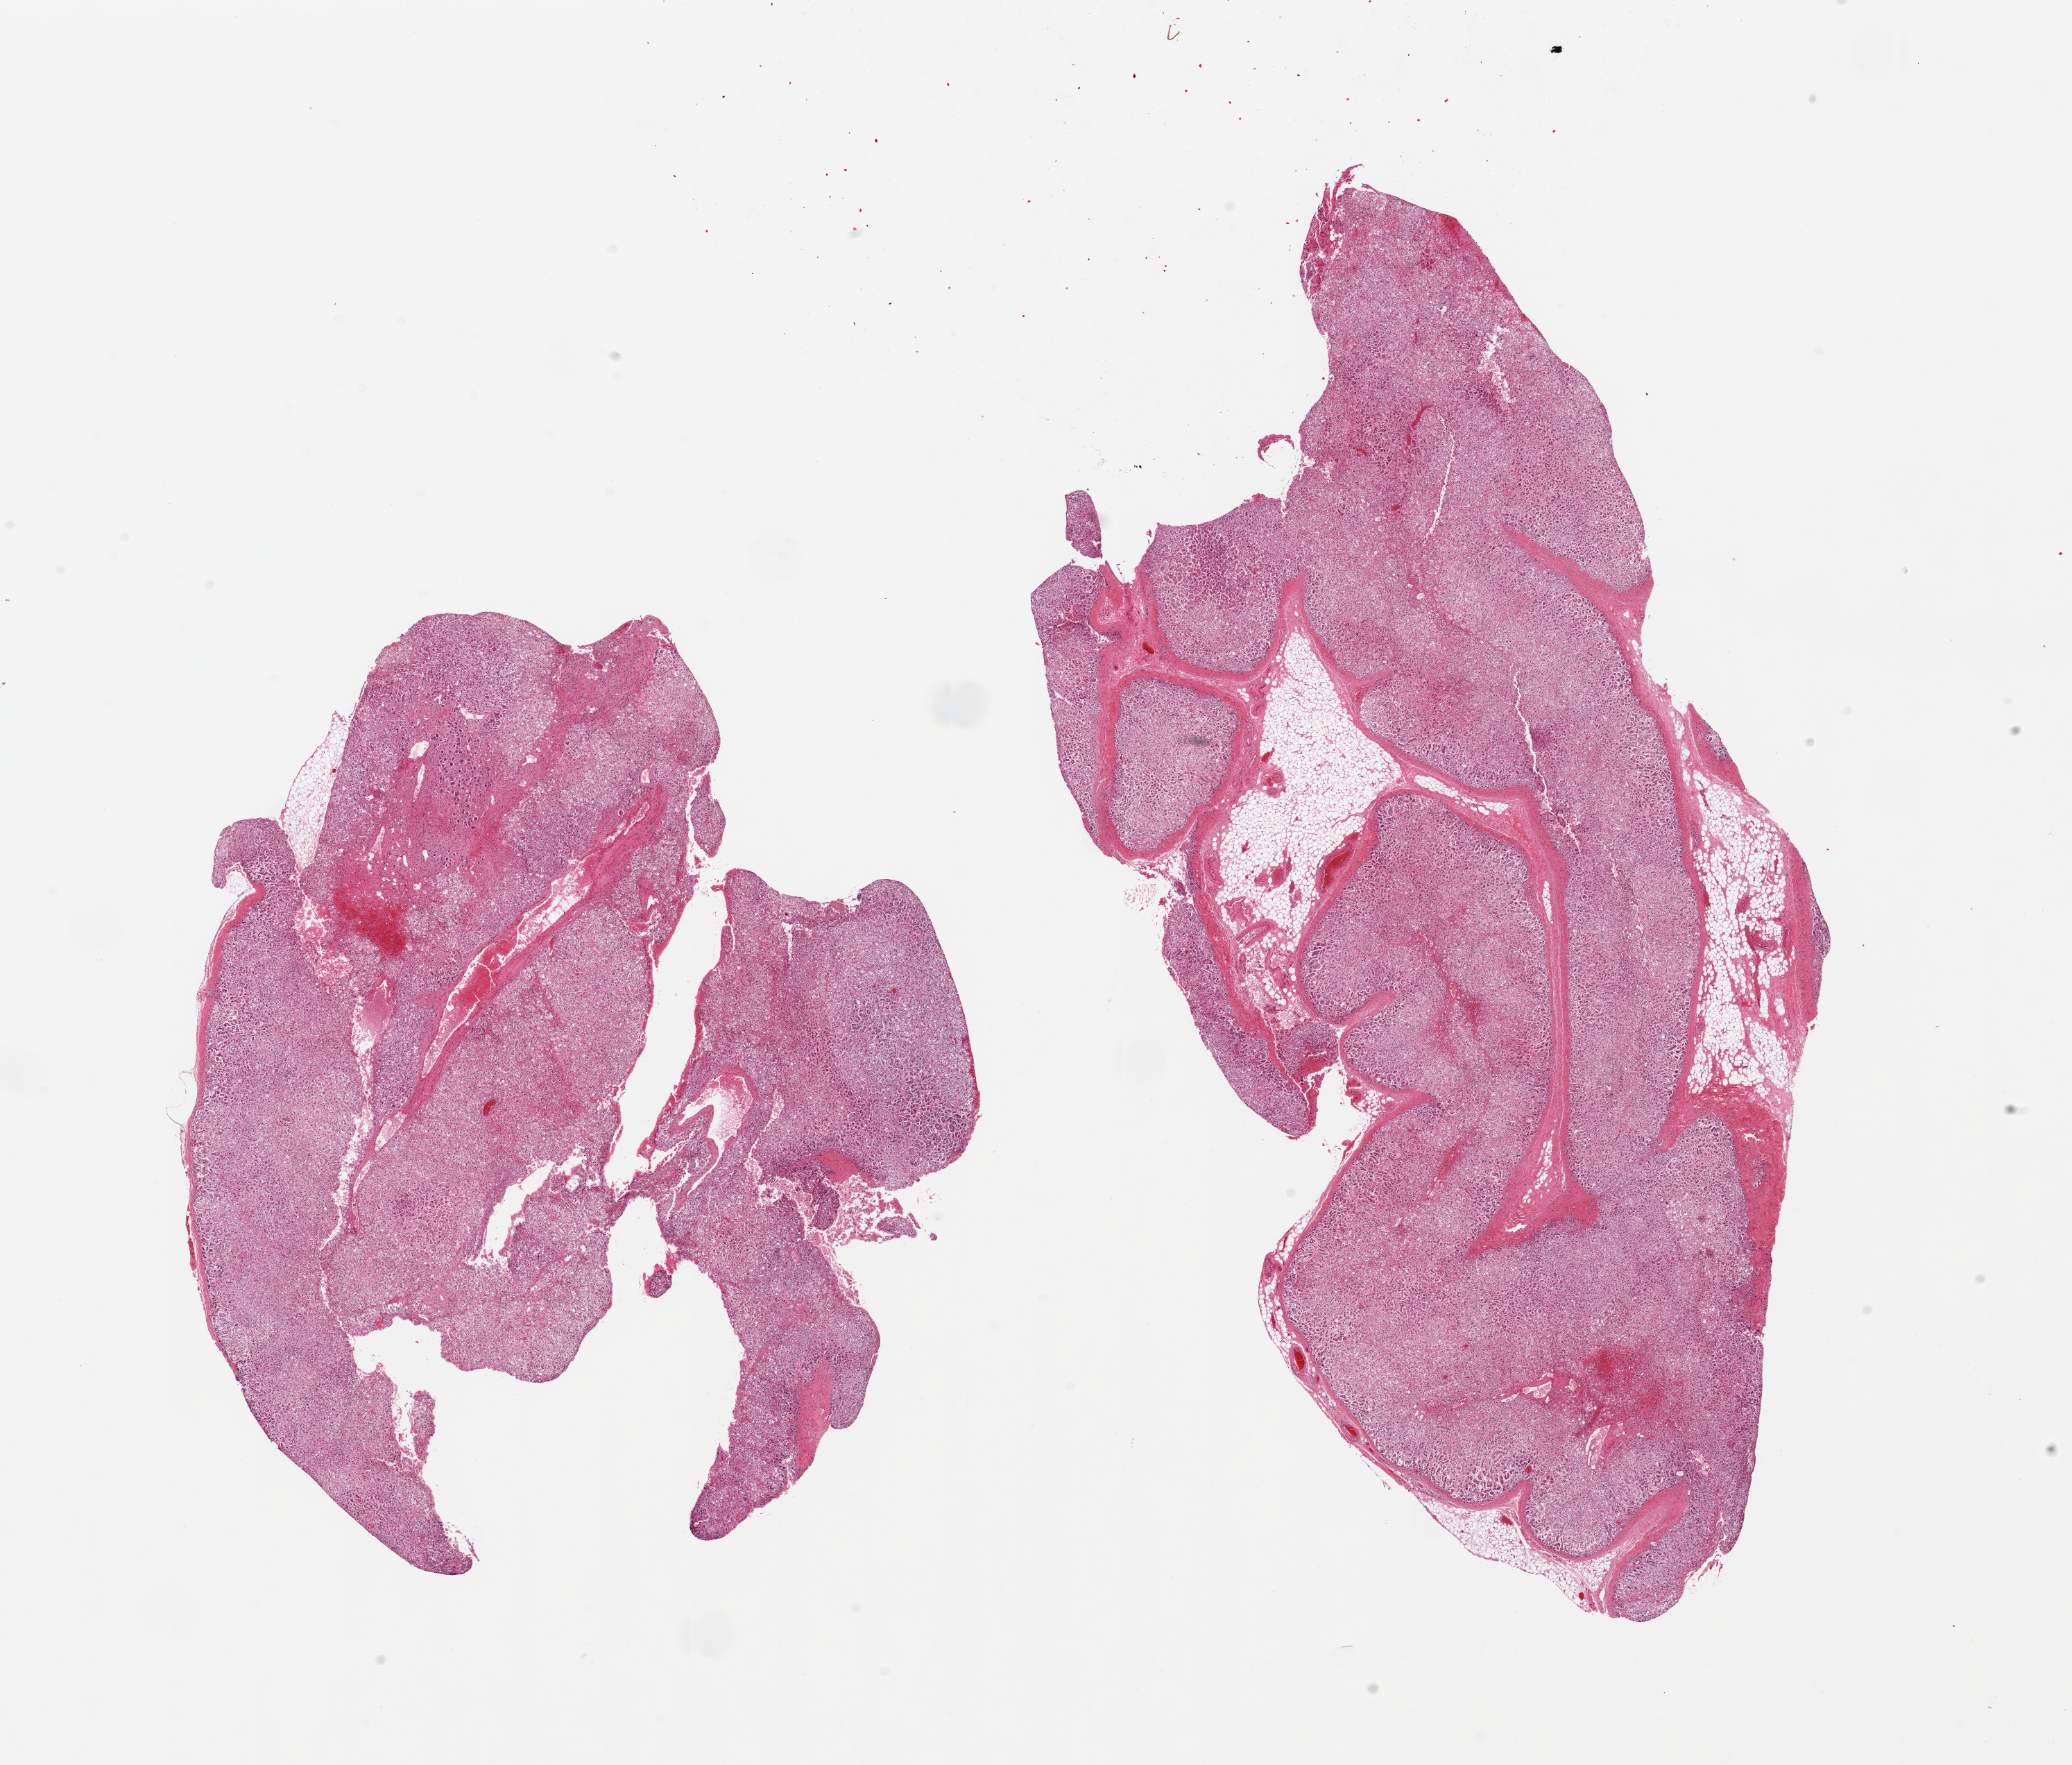
Whole-slide image, H&E stain — a low-resolution overview of the entire scanned area, about 23.6 x 20.1 mm (acquisition: 20x scan). PAXgene-fixed, paraffin-embedded tissue. Sampled site (target tissue): adrenal gland. Donor tissue sample. Donor sex: male.
Reviewer comment on this tissue sample: 2 pieces, all cortex, advanced autolysis; adherent fat is ~15% total.